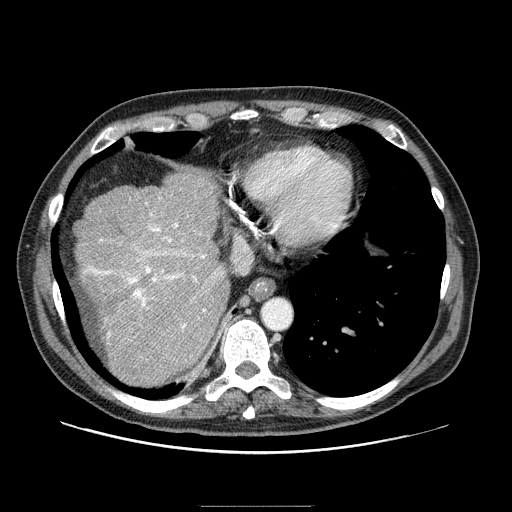
Contrast-enhanced abdominal CT (liver protocol), one axial slice; one of 2 acquisitions stored at this slice position; soft-tissue window (W 400 / L 40 HU); 2.5 mm slice thickness; 512 × 512 image matrix, field of view 400 × 400 mm. From the clinical record (not read from this slice): diagnosis: hepatocellular carcinoma (patient treated with transarterial chemoembolisation; whether this scan precedes or follows treatment is not stated here); TNM stage (as recorded): Stage-II; Child-Pugh class: A; tumour nodularity: multinodular.
Annotated regions visible in this slice (semi-automatic segmentation, software-assisted and operator-edited):
- abdominal aorta: box from (x=261, y=298) to (x=292, y=329) px
- liver parenchyma outside the tumour (the mass and vessels are separate outlines, so this box may not span the whole liver): (x=74, y=168)–(x=230, y=384)
- liver vessels: (x=86, y=198)–(x=223, y=337)